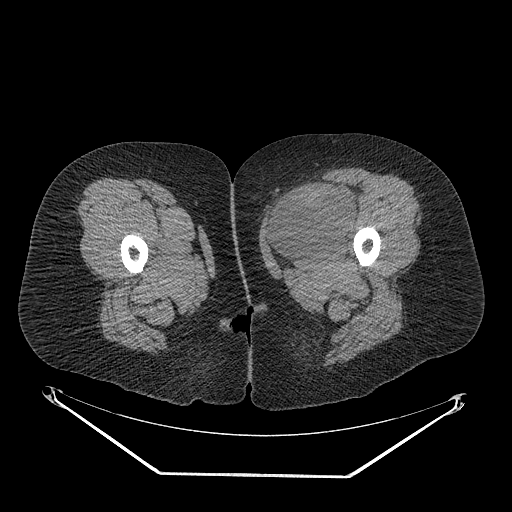
CT of an extremity soft-tissue mass (from a PET/CT study), one axial slice; position 27 of 267 along the scan axis; reconstruction kernel STANDARD; 140 kVp; soft-tissue window (W 400 / L 40 HU); 3.75 mm slice thickness; 512 × 512 image matrix. Female patient. From the clinical record (not read from this slice): histological type: myxofibrosarcoma; grade: intermediate; site of the primary tumour: left thigh.
Annotated regions visible in this slice (expert contour drawn on MRI and transferred to this co-registered scan by the dataset authors):
- gross tumour volume including surrounding oedema: bounding box [x1, y1, x2, y2] px = [265, 185, 357, 259]
- gross tumour volume (mass): [267, 189, 353, 254]